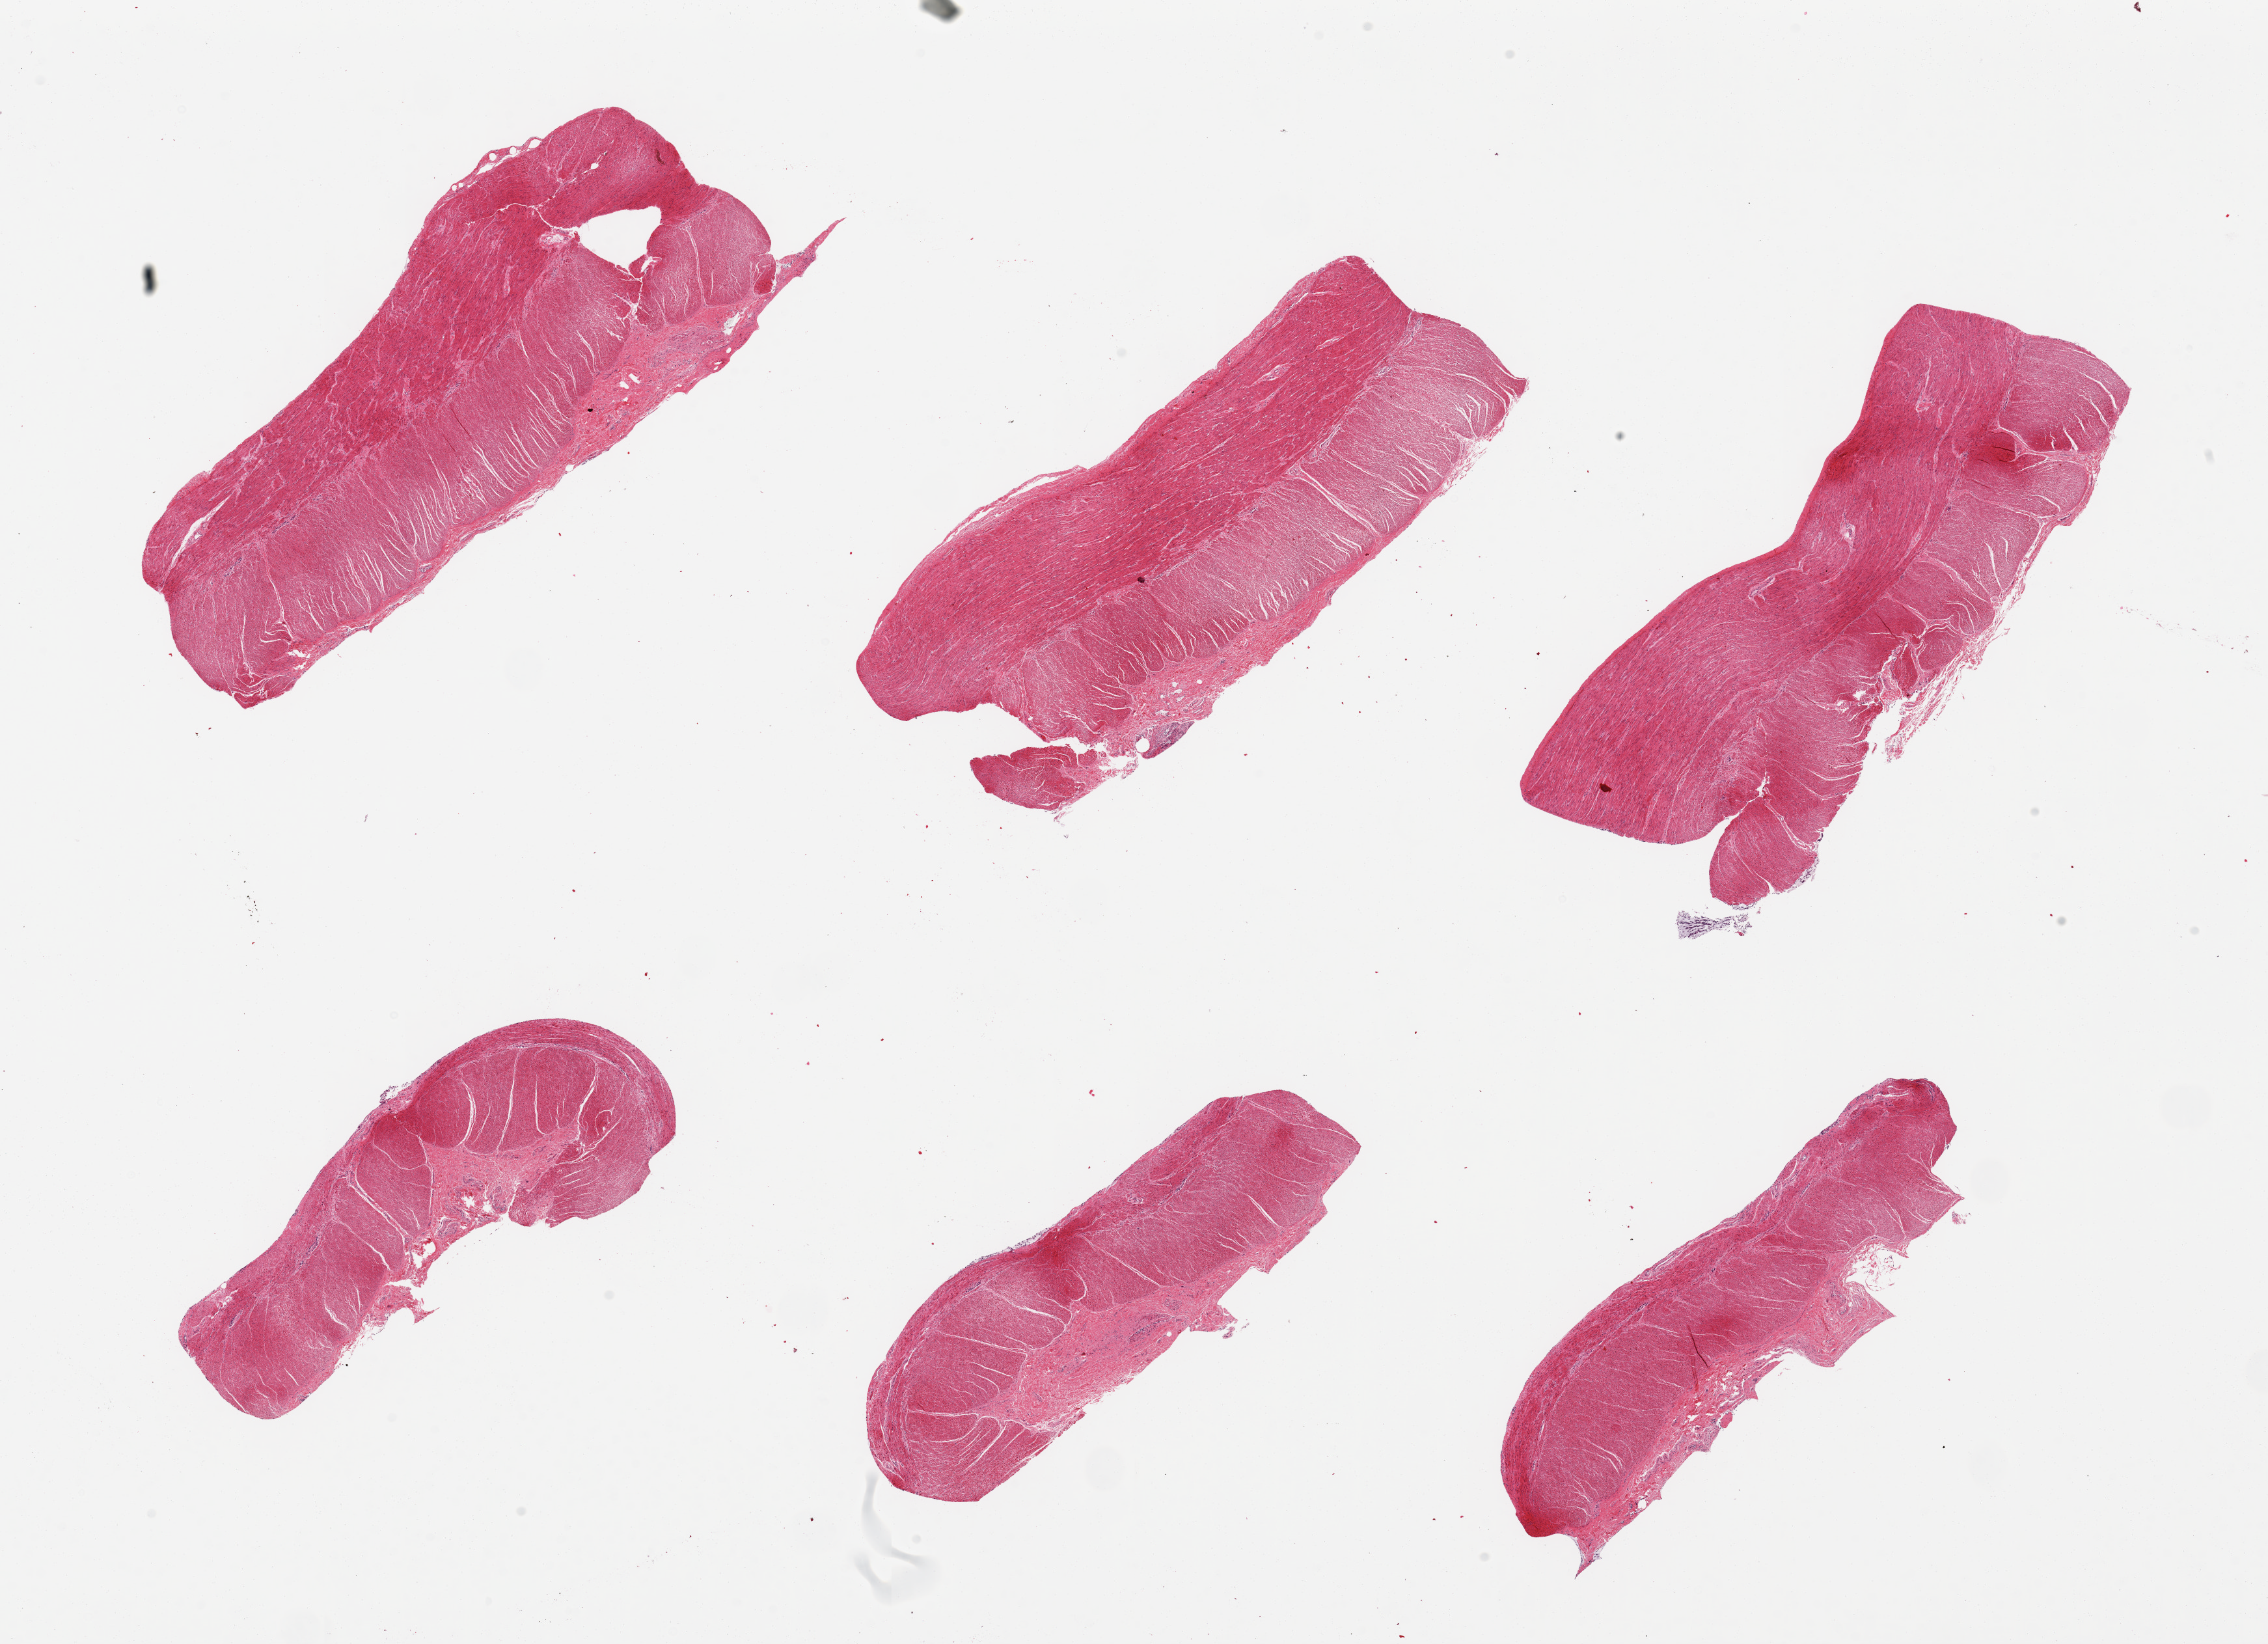
H&E whole-slide image — a low-resolution overview of the entire scanned area, about 27.6 x 20.0 mm; PAXgene-fixed paraffin-embedded (PFPE) section; target tissue: sigmoid colon; donor tissue sample. Donor: female.
Review note (as recorded): 6 pieces.